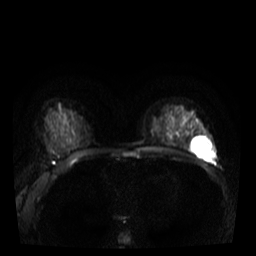
Breast MRI, one axial slice. Position 21 of 40 along the scan axis. Diffusion-weighted series; image 2 of 4 stored at this slice position (different b-values; order by instance number). 3 T. 5 mm slice thickness. 256 × 256 image matrix, field of view 320 × 320 mm. Female patient.
Annotated regions visible in this slice (manually delineated by an expert):
- tumour on diffusion-weighted imaging: bounding box [x1, y1, x2, y2] px = [207, 141, 210, 147]